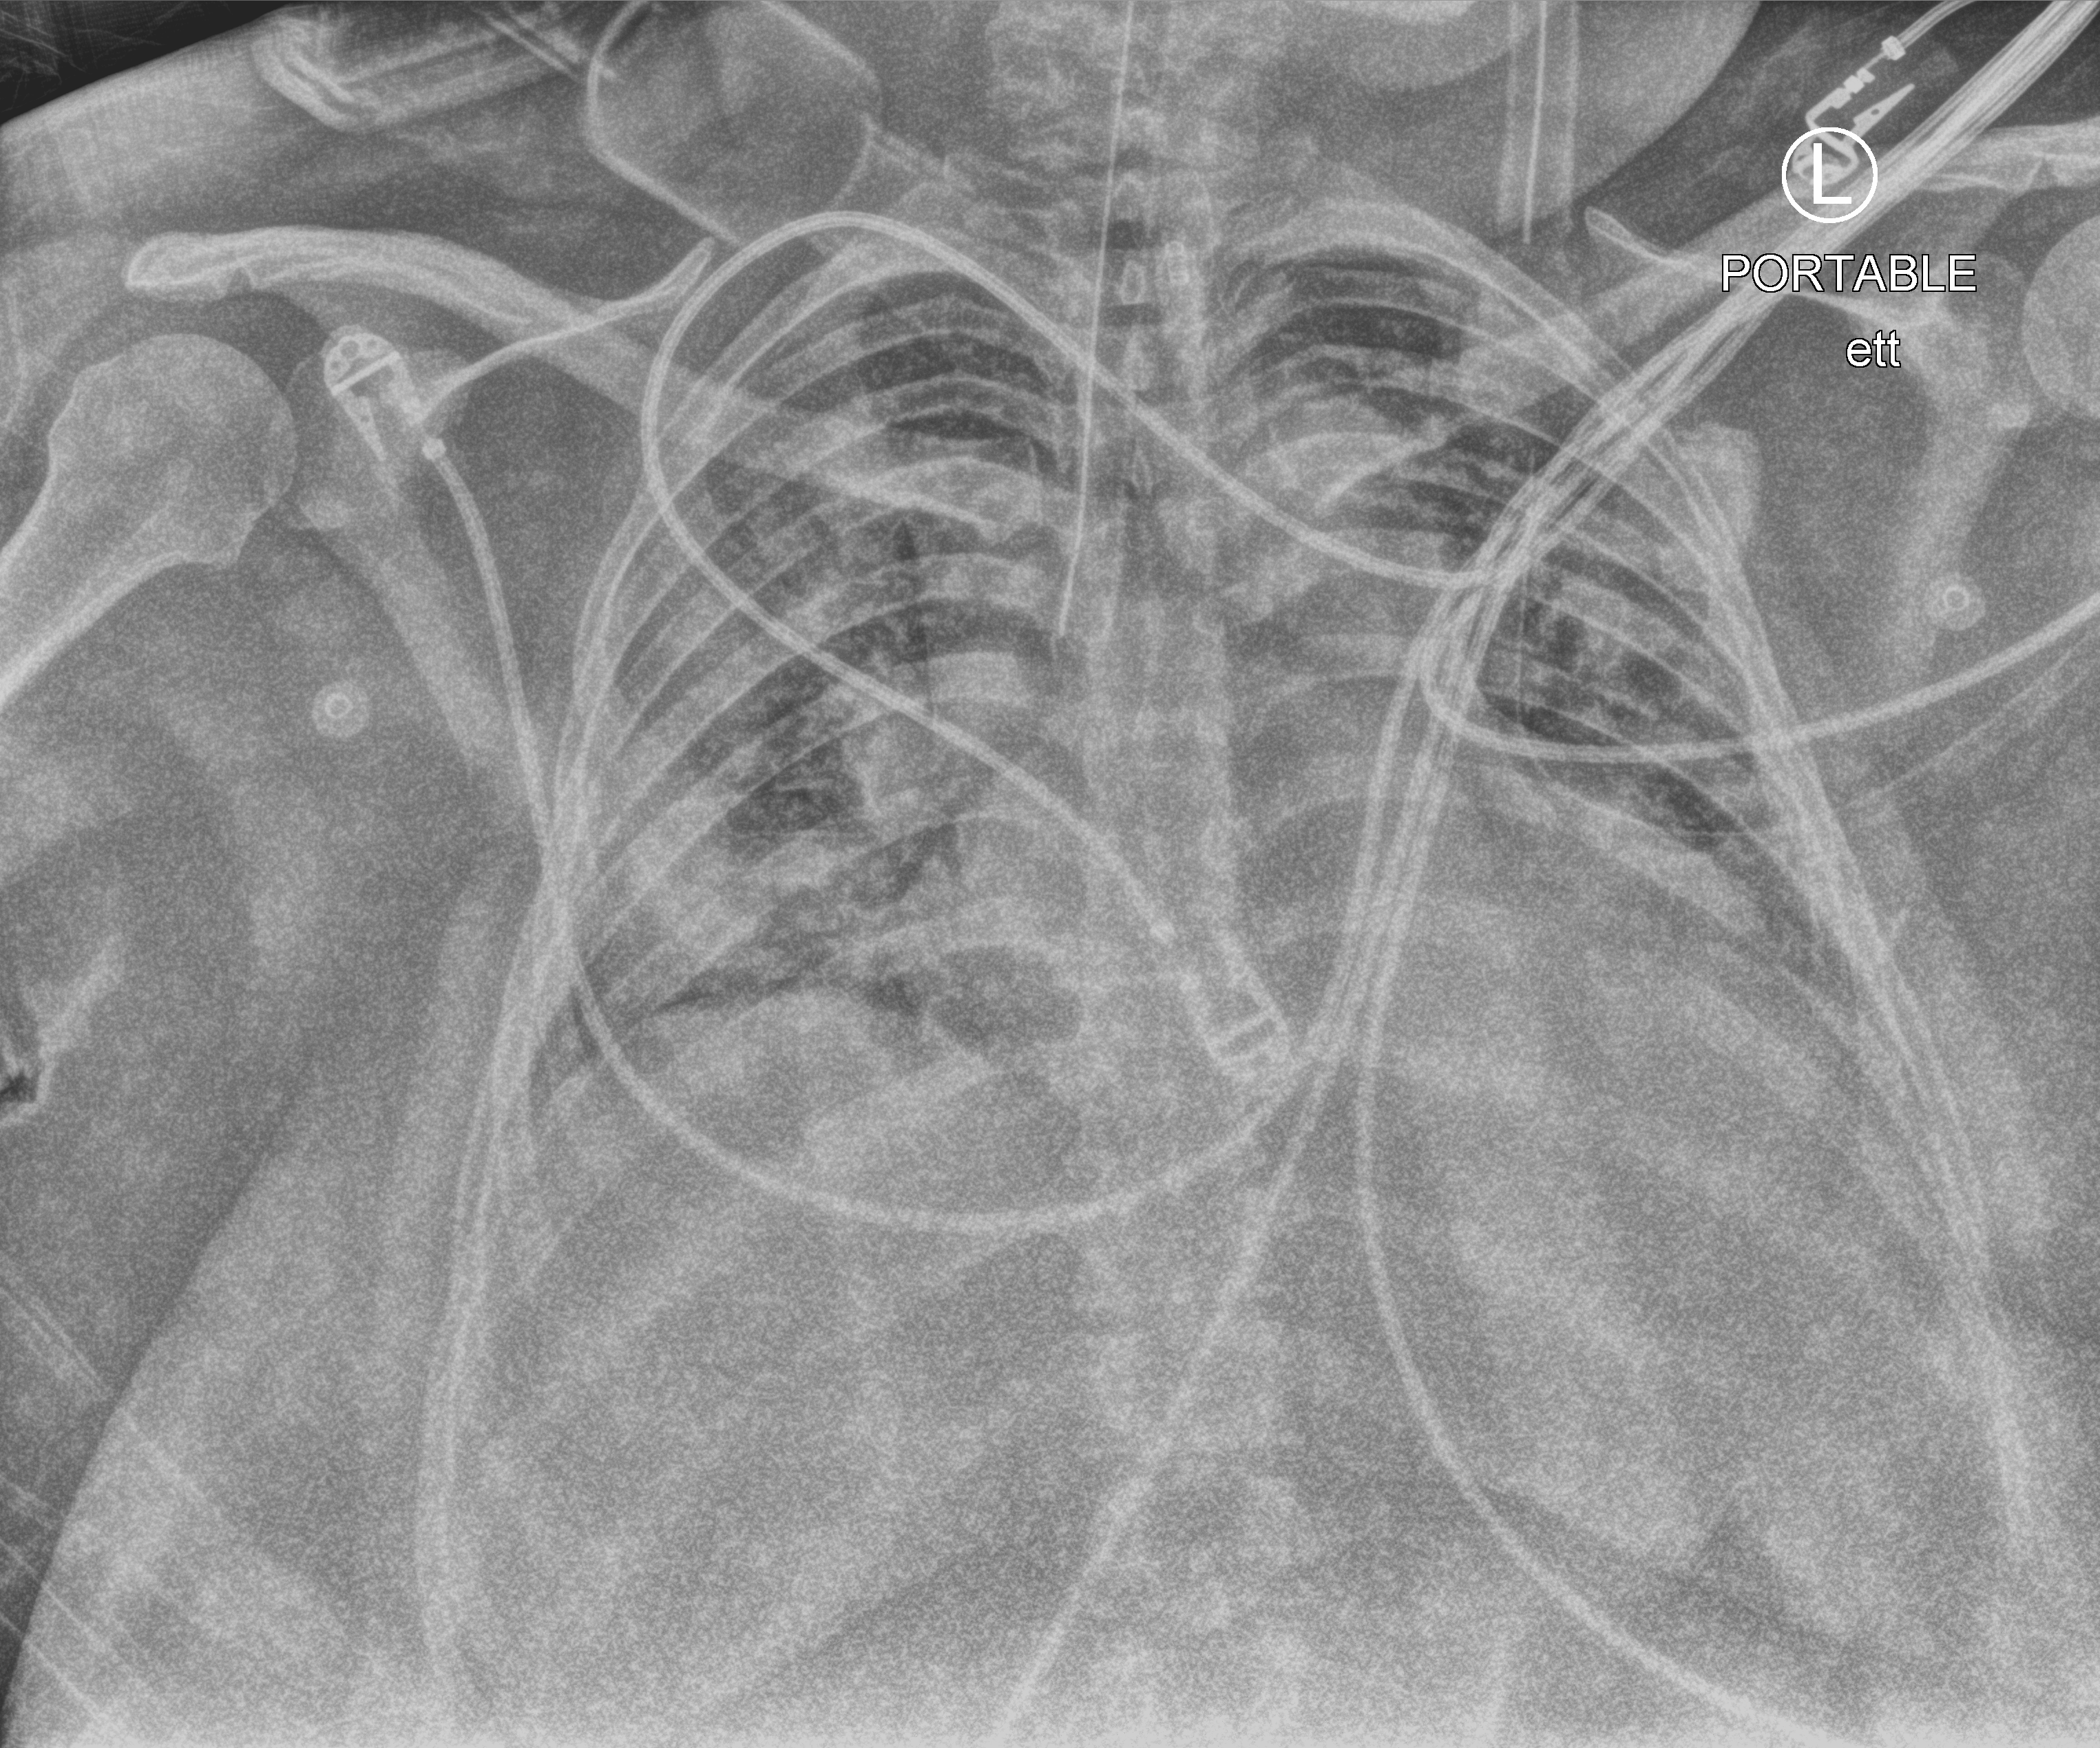
Chest X-ray (portable). Patient hospitalised with COVID-19; female, aged 18–59 years.
Hospital-stay facts (about this admission, not read from this image; timing relative to this image not recorded):
- admitted to intensive care during this hospital stay: yes
- hypertension (admission record): no
- COPD (admission record): no